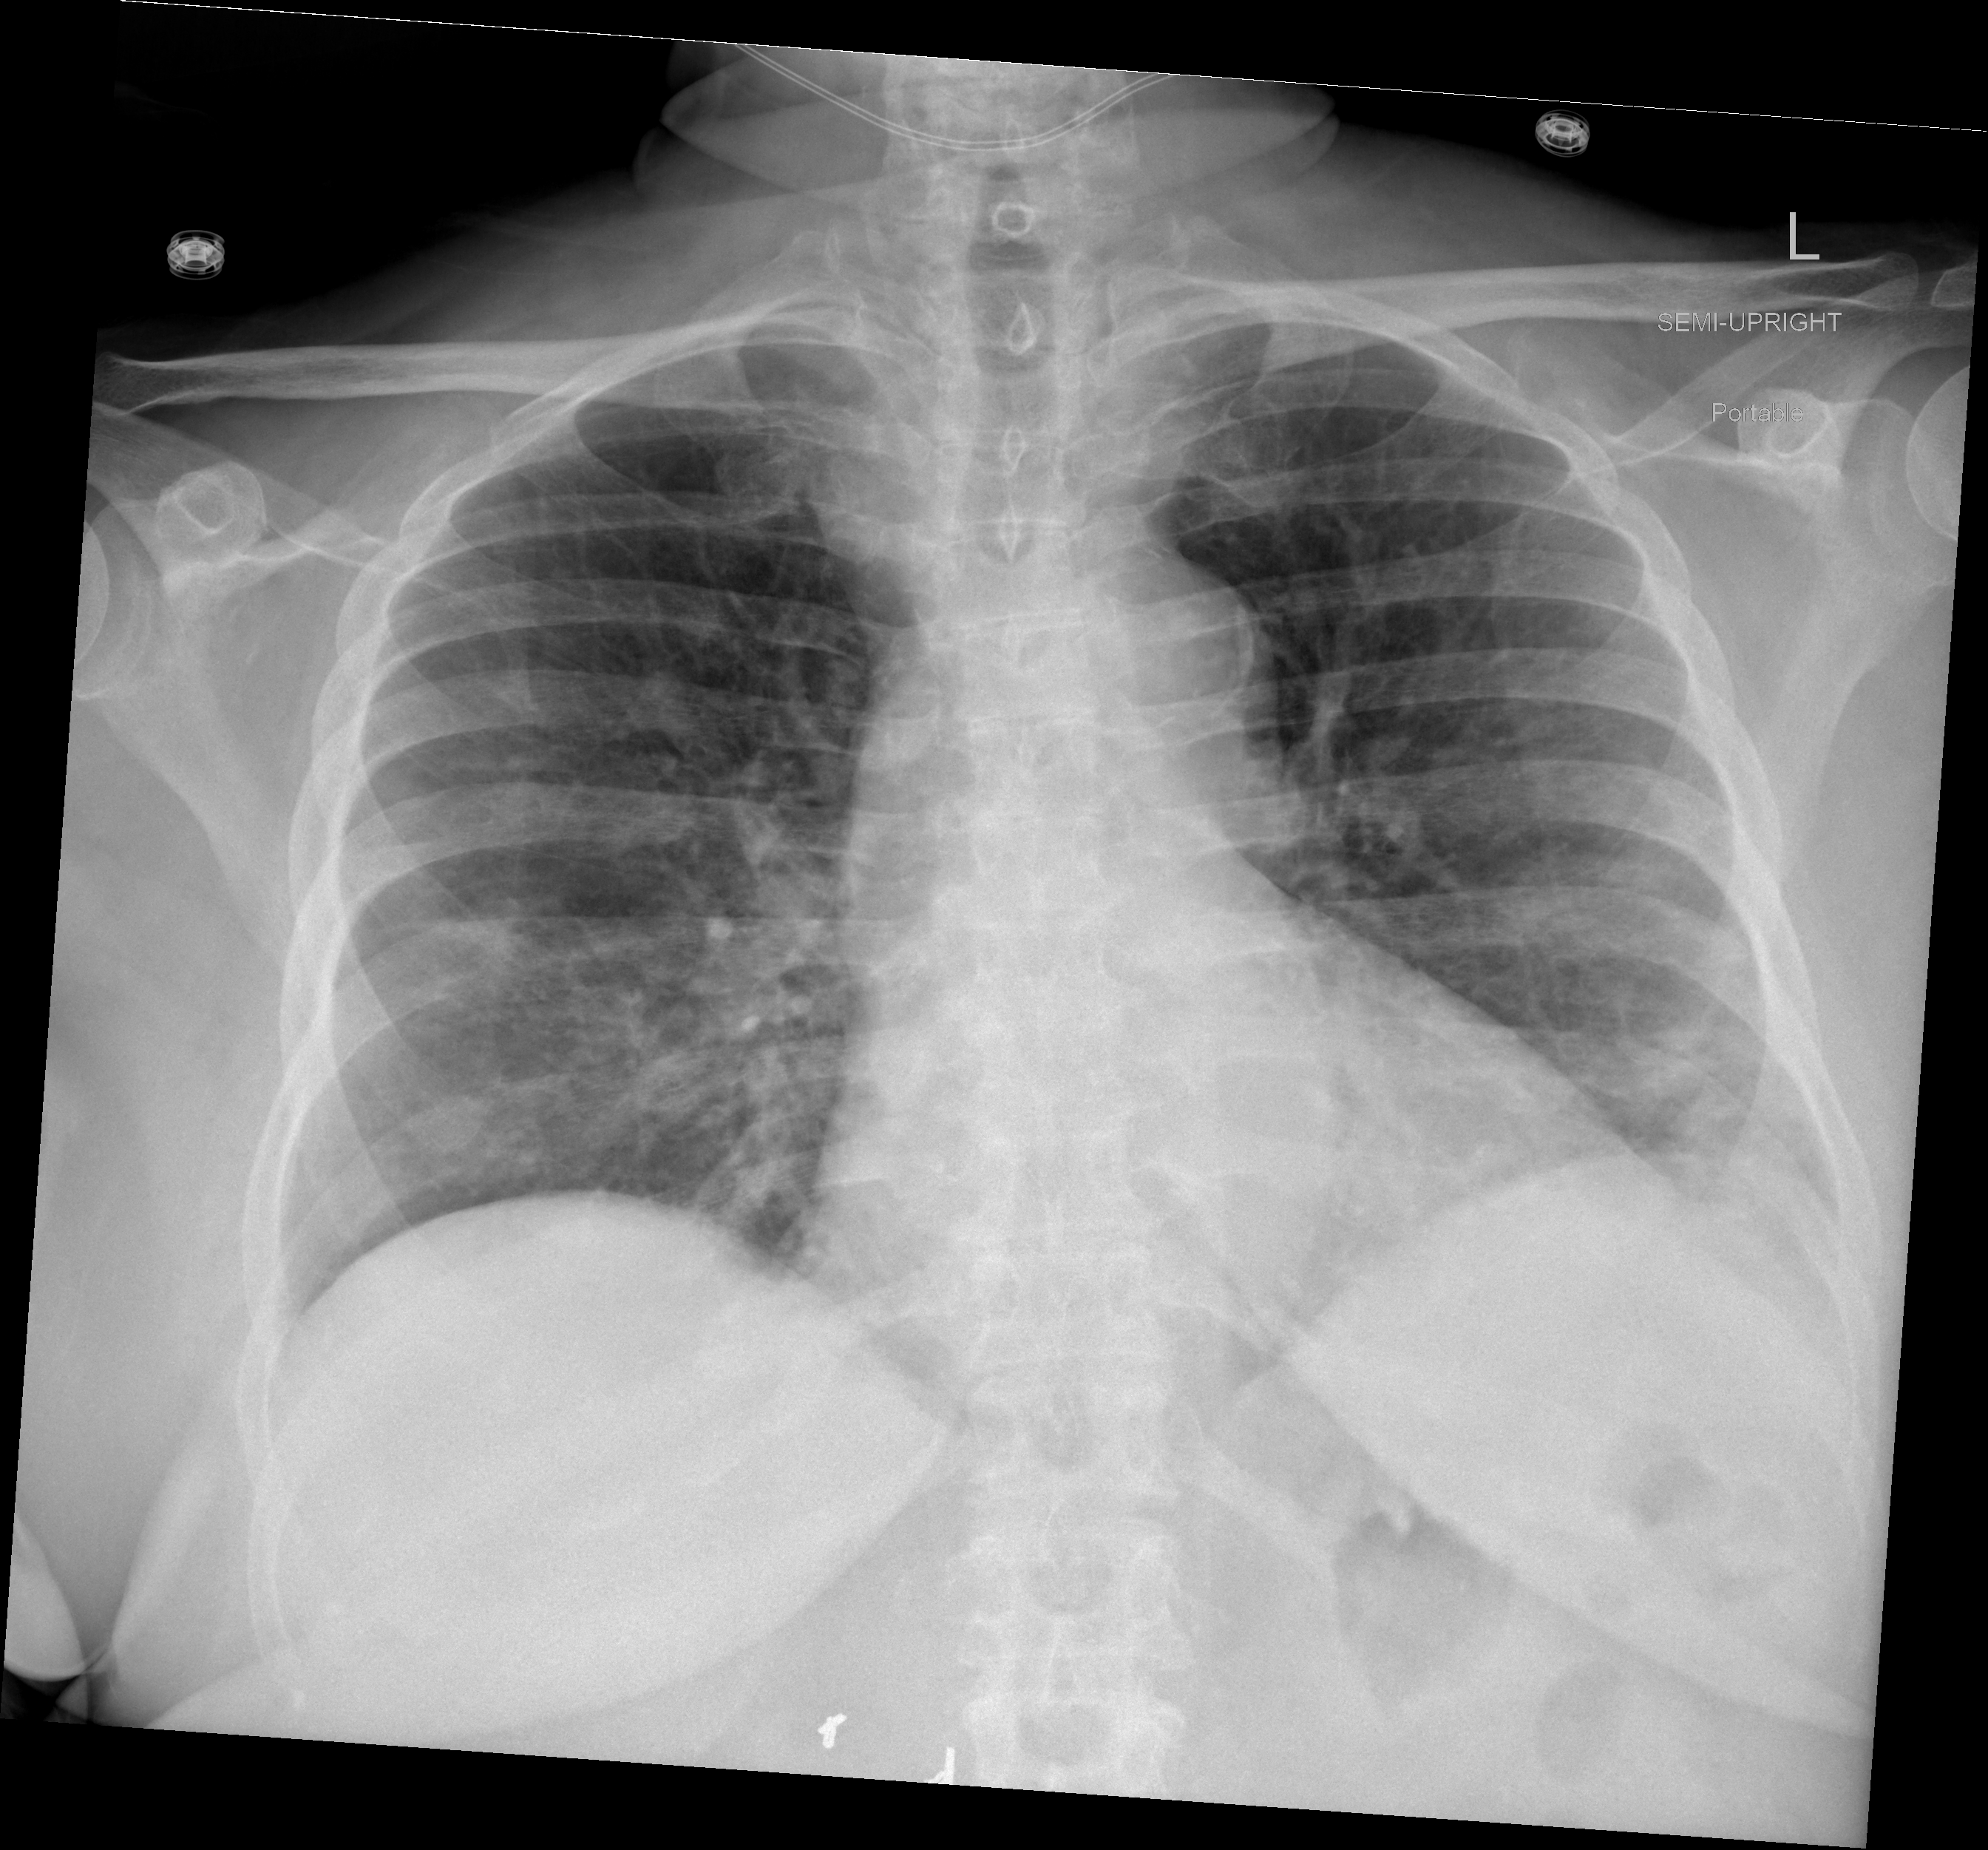
Chest X-ray (portable), AP projection. Female patient, age 65 years; imaged 0 days after the COVID-19 diagnosis.
Radiologist key findings (as recorded): The lungs are free of air space disease.